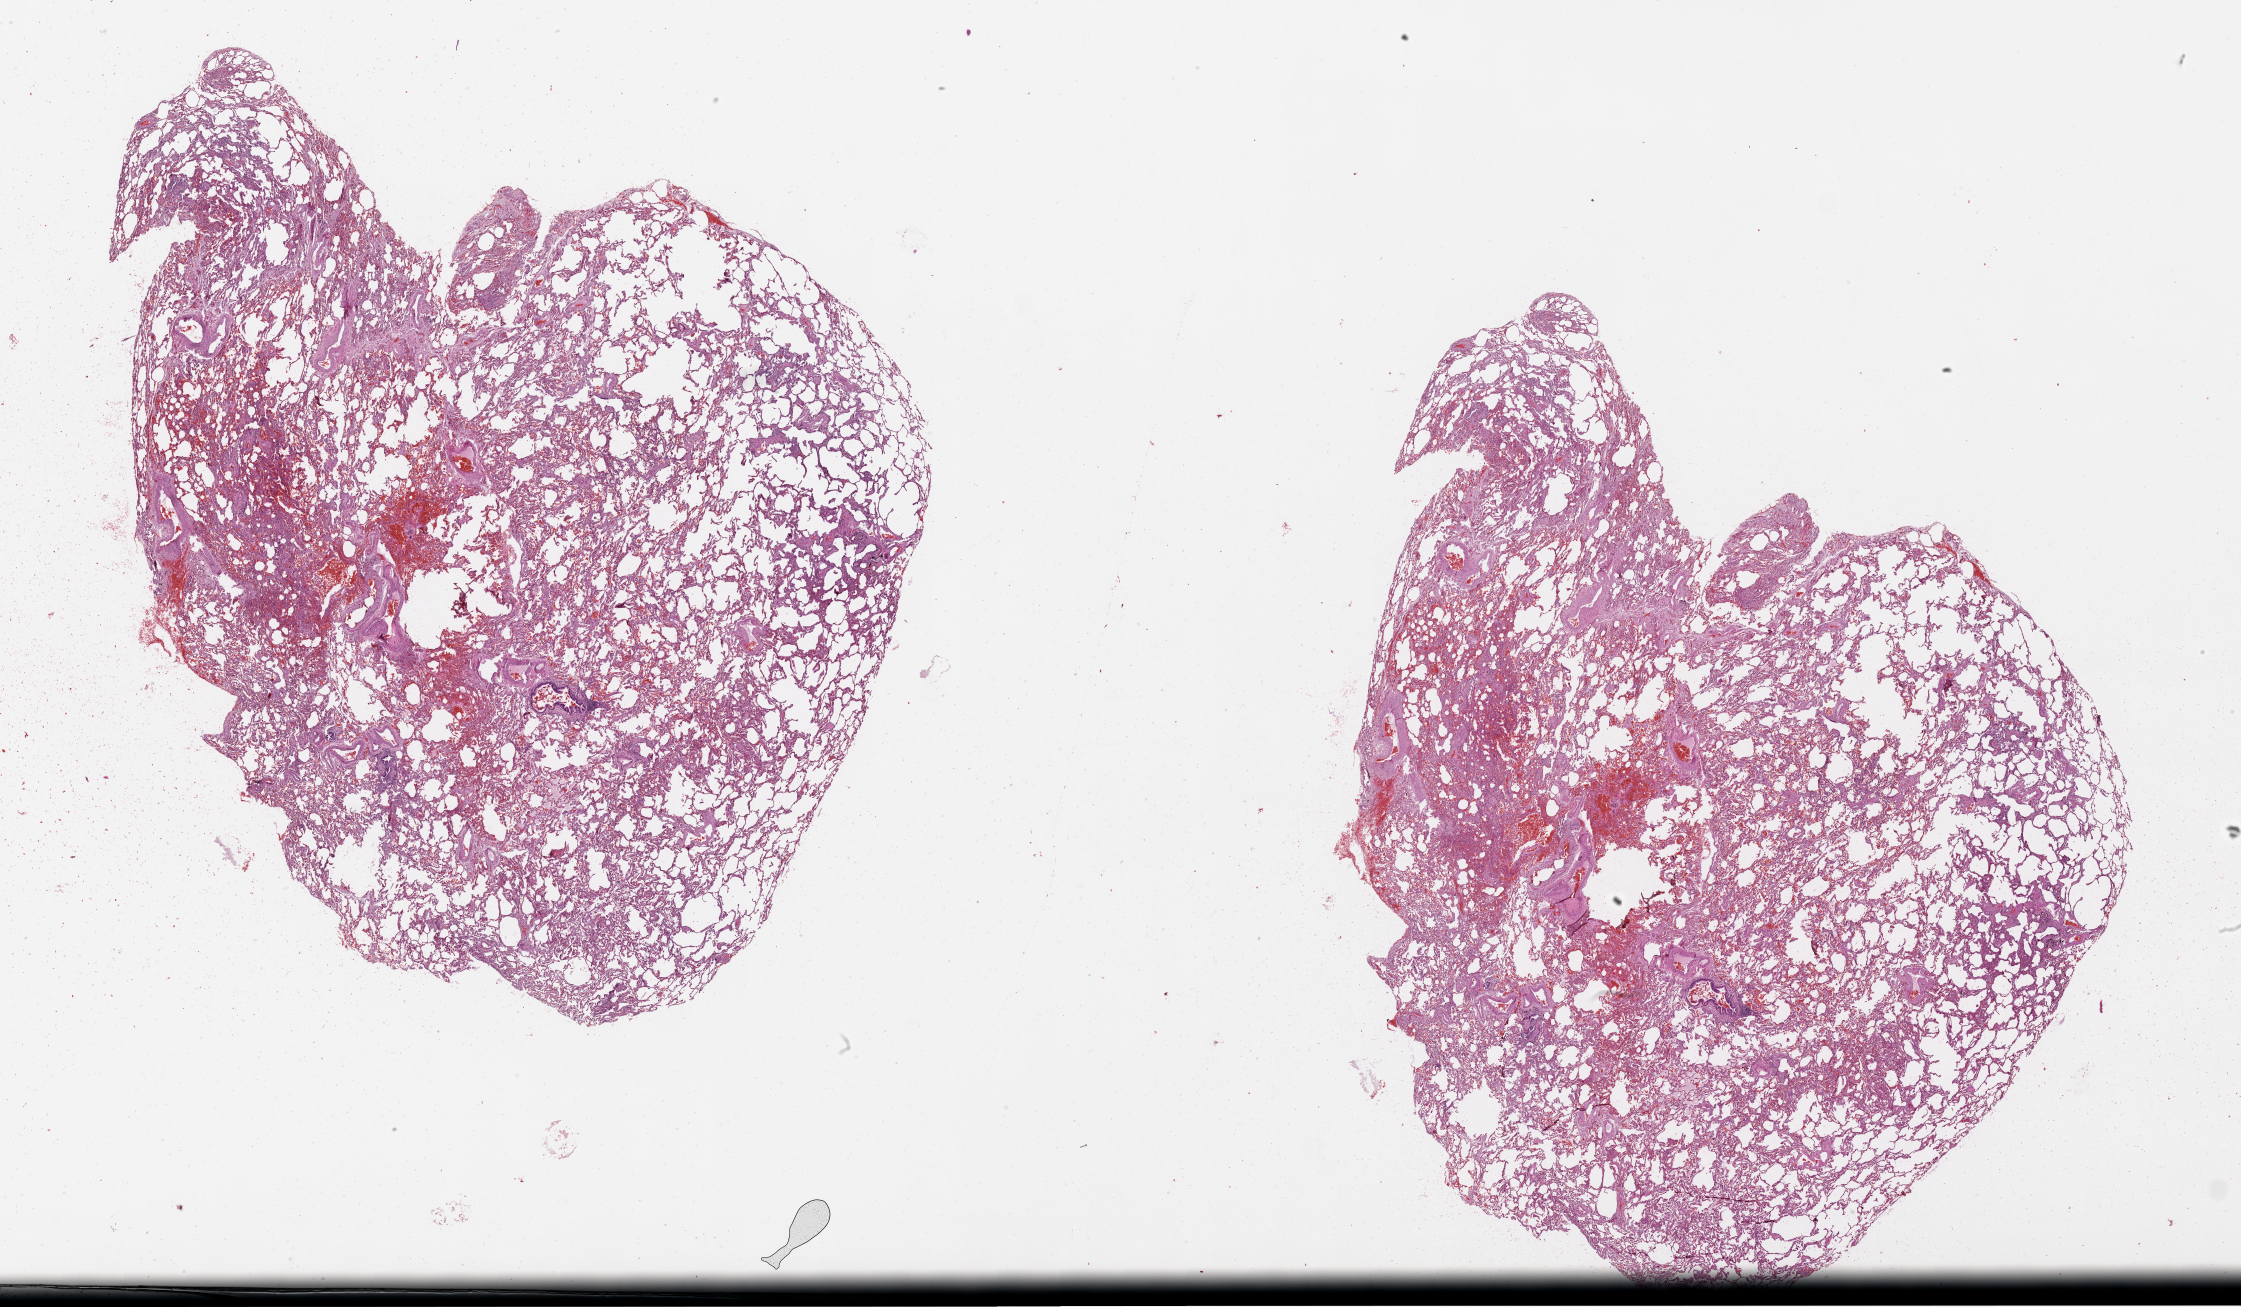
Whole-slide histology image, H&E, whole scanned area (about 36.1 x 21.0 mm) shown as a low-resolution overview. Lung, normal (non-tumour) tissue. Female, 62 y/o.
This section: normal (non-tumour) tissue from the same patient. Patient diagnosis (cohort enrolment): squamous cell carcinoma (lung).